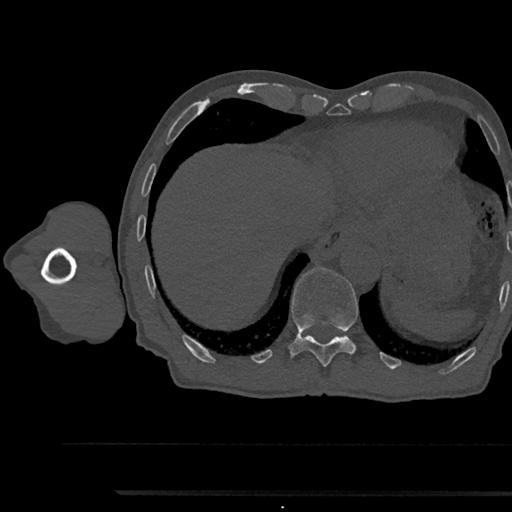
CT including the spine, one axial slice. Position 784 of 797 along the scan axis. Reconstruction kernel Br40s/3. 120 kVp. Bone window (W 1800 / L 400 HU). 0.5 mm slice thickness. 512 × 512 image matrix, field of view 367 × 367 mm. Male patient, age 79 years. From the clinical record (not read from this slice): primary cancer: prostate.
Outlined on this slice (semi-automatically segmented with operator editing):
- T11 vertebra: bounding box [x1, y1, x2, y2] px = [289, 267, 358, 367]